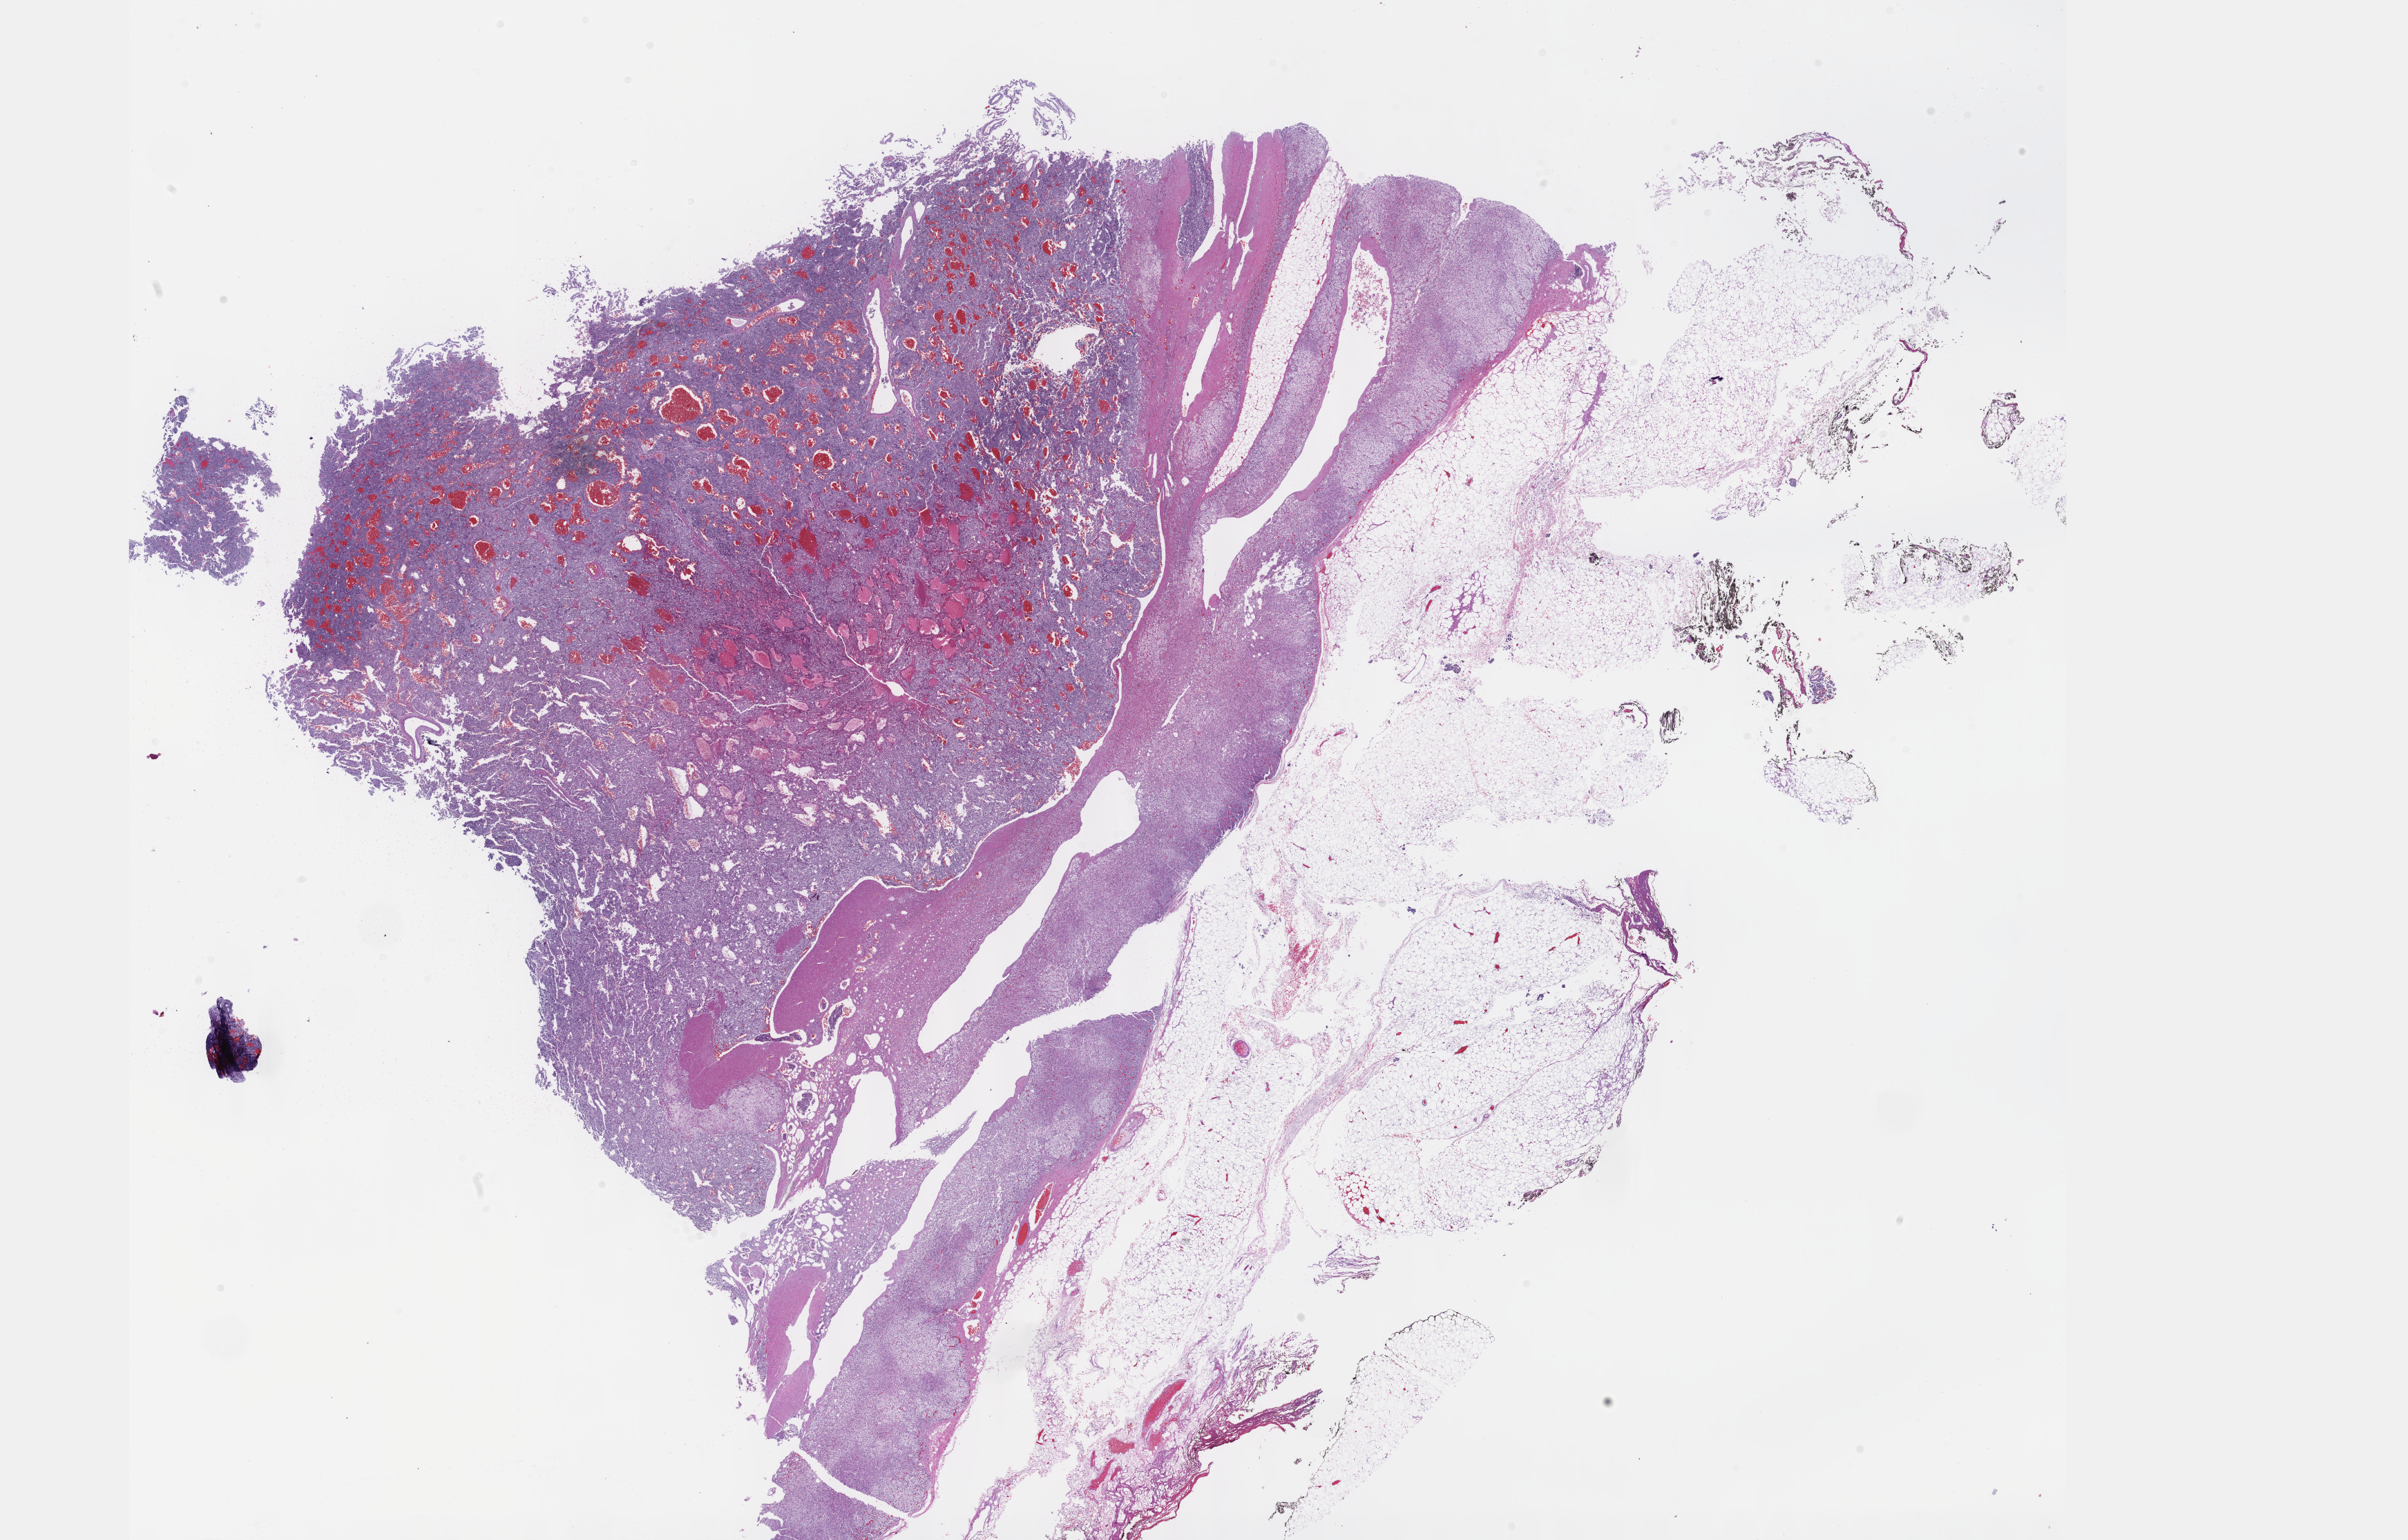
Whole-slide histology image, Hematoxylin and eosin (H&E) stained, a low-resolution overview of the entire scanned area, about 28.2 x 18.0 mm (from a 40x scan). Formalin-fixed paraffin-embedded (FFPE) diagnostic section. Primary tumour sample from the adrenal gland. Male, age 43 years at initial diagnosis.
Histologic diagnosis: Pheochromocytoma, NOS. Laterality: right.